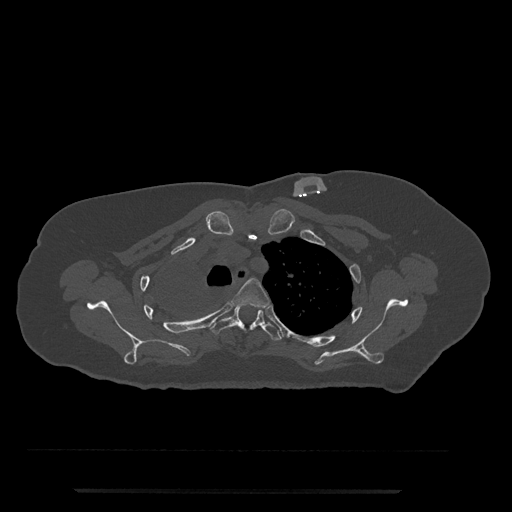
CT including the spine, one axial slice. Slice 608 of 797 in the series (ordered by position). Bone window (W 1800 / L 400 HU). 0.5 mm slice thickness. 512 × 512 image matrix. Patient: female, 51 years. Case-level facts recorded for this patient, not image findings: primary cancer: neuro.
Structures marked on this image (semi-automatically segmented with operator editing):
- T3 vertebra: box from (x=233, y=278) to (x=270, y=309) px
- T4 vertebra: (x=210, y=306)–(x=282, y=341)